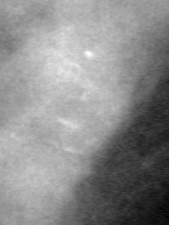
Crop from a digitized film mammogram around one marked abnormality; right breast; MLO view; BI-RADS breast density category 4 (scale 1–4).
Finding: calcifications, morphology pleomorphic, distribution clustered; BI-RADS assessment category 4; pathology (as recorded): benign.